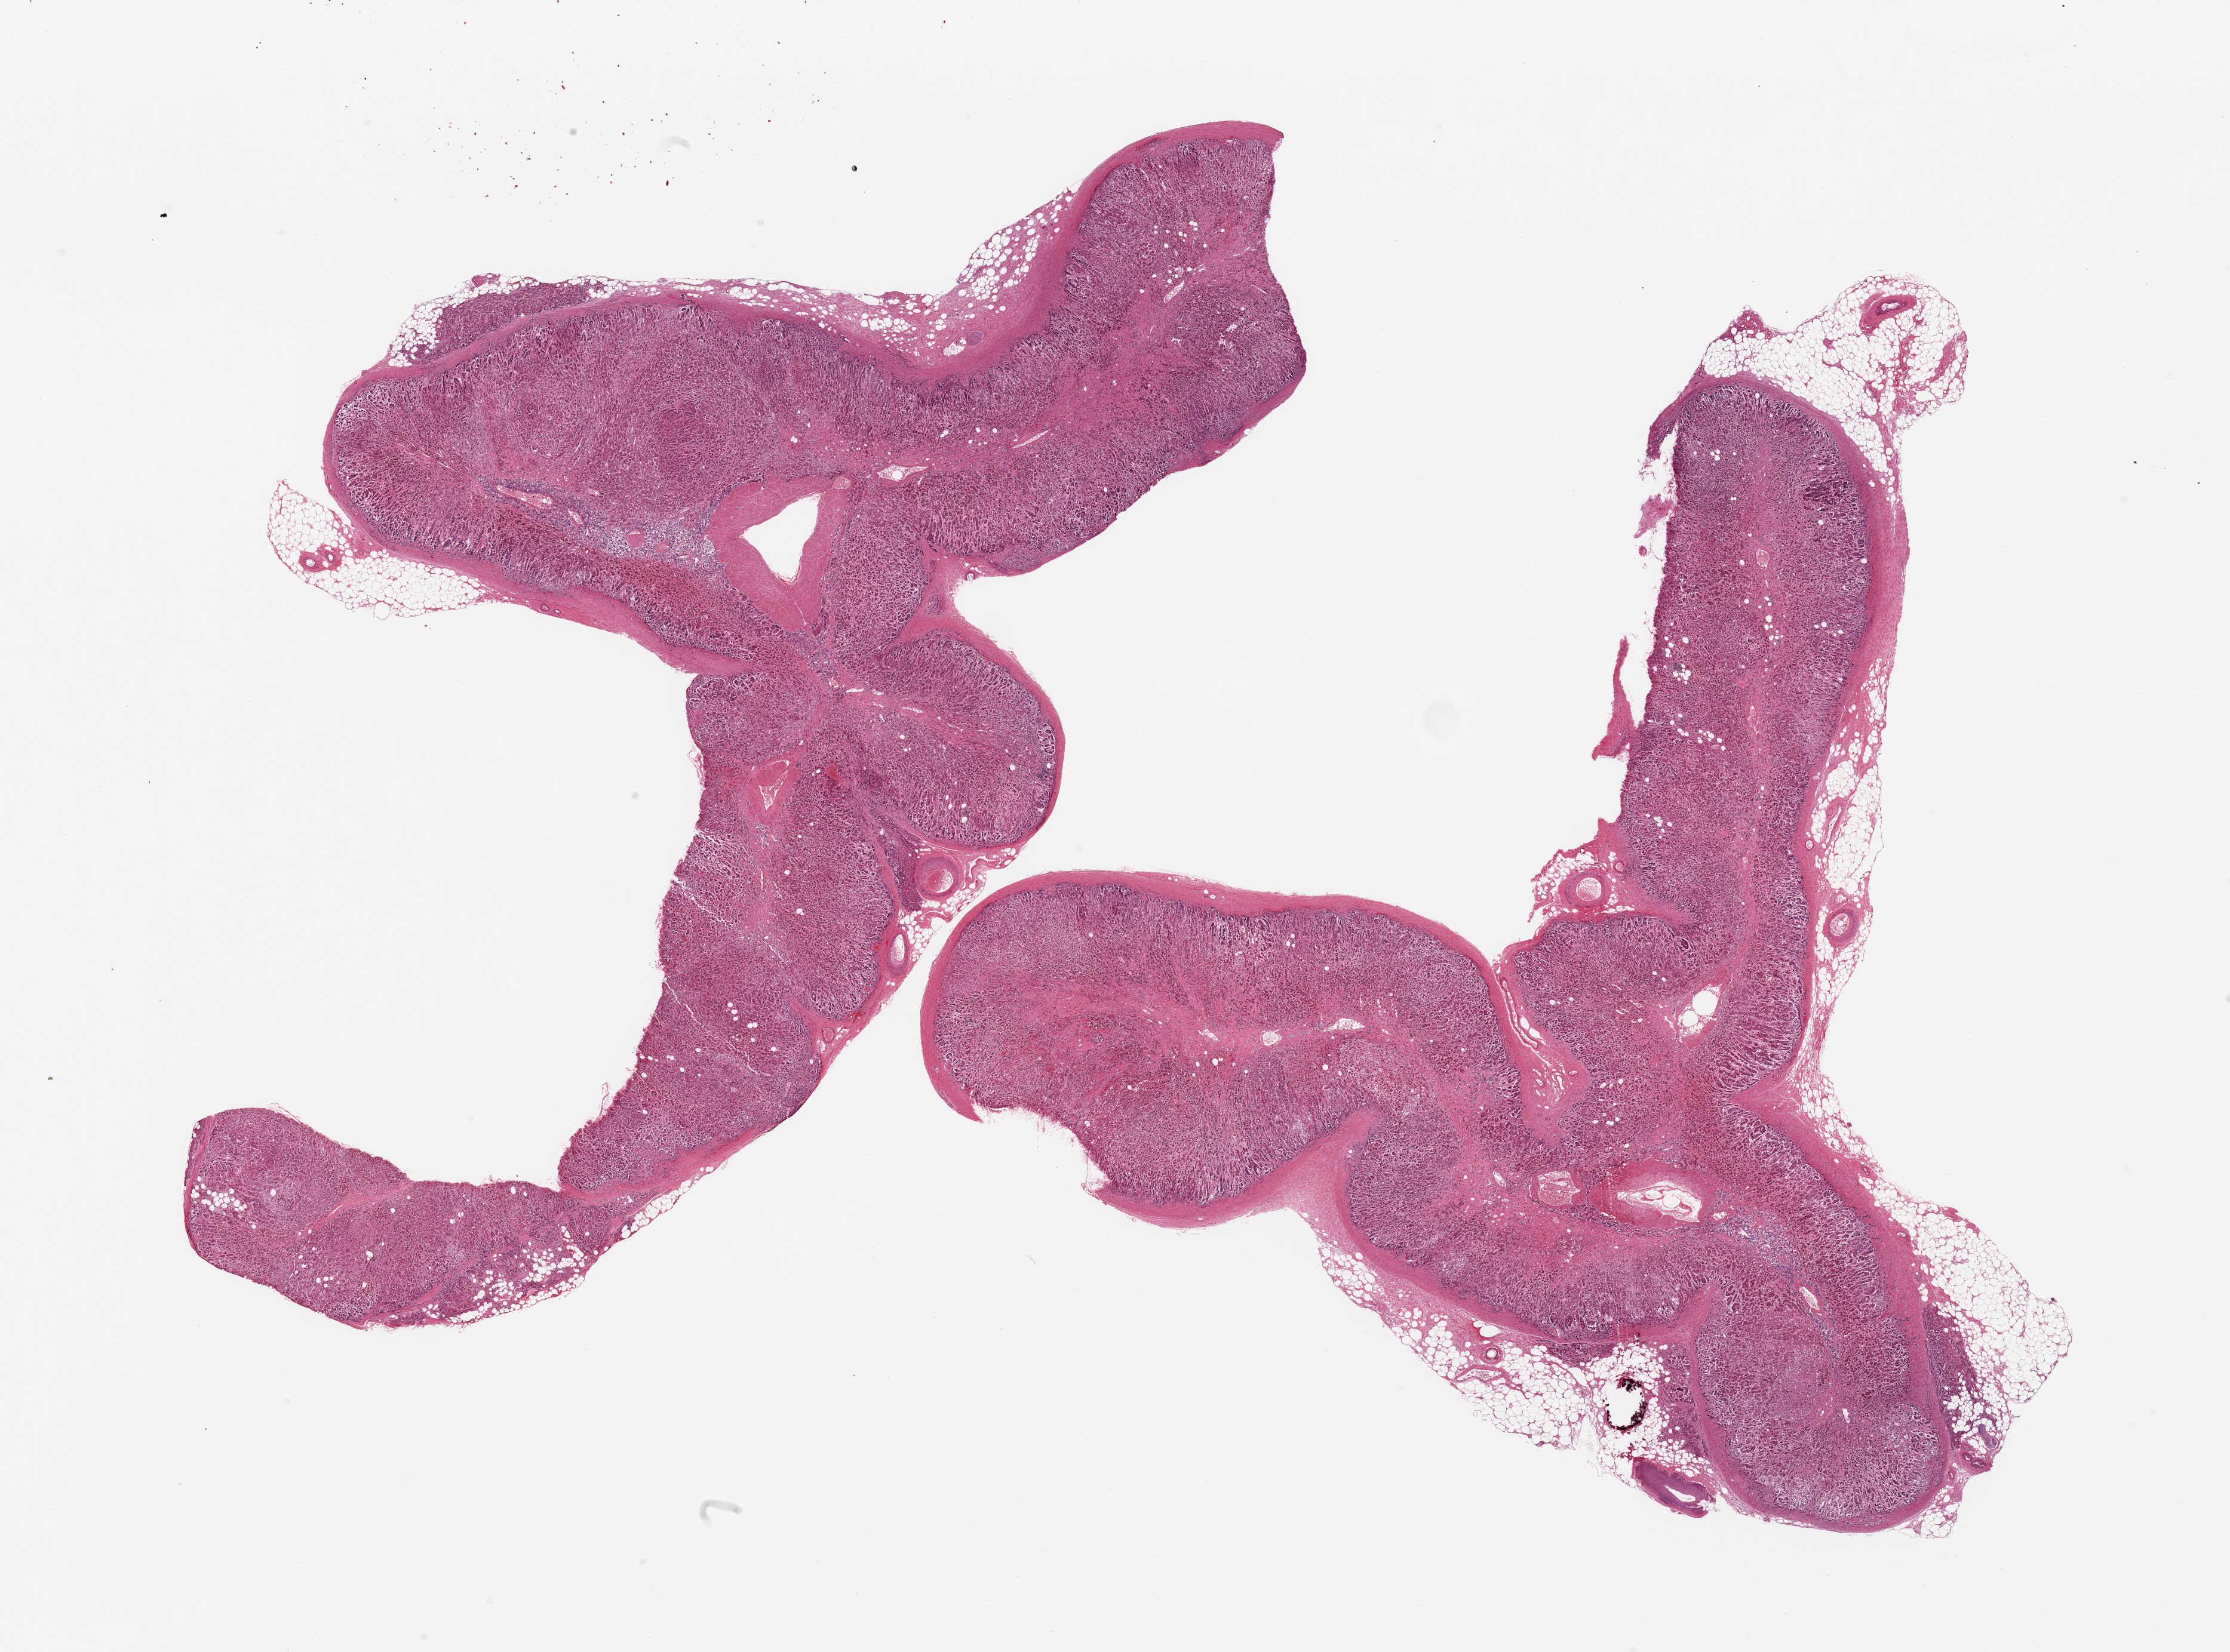
Whole-slide image, haematoxylin and eosin stain, a low-resolution overview of the entire scanned area, about 29.5 x 21.9 mm (from a 20x scan). PAXgene-fixed paraffin-embedded (PFPE) section. Sampled site (target tissue): adrenal gland. Donor tissue sample. Male donor.
Reviewer comment on this tissue sample: 2 pieces, mainly cortex, foci of medulla up to 3mm.